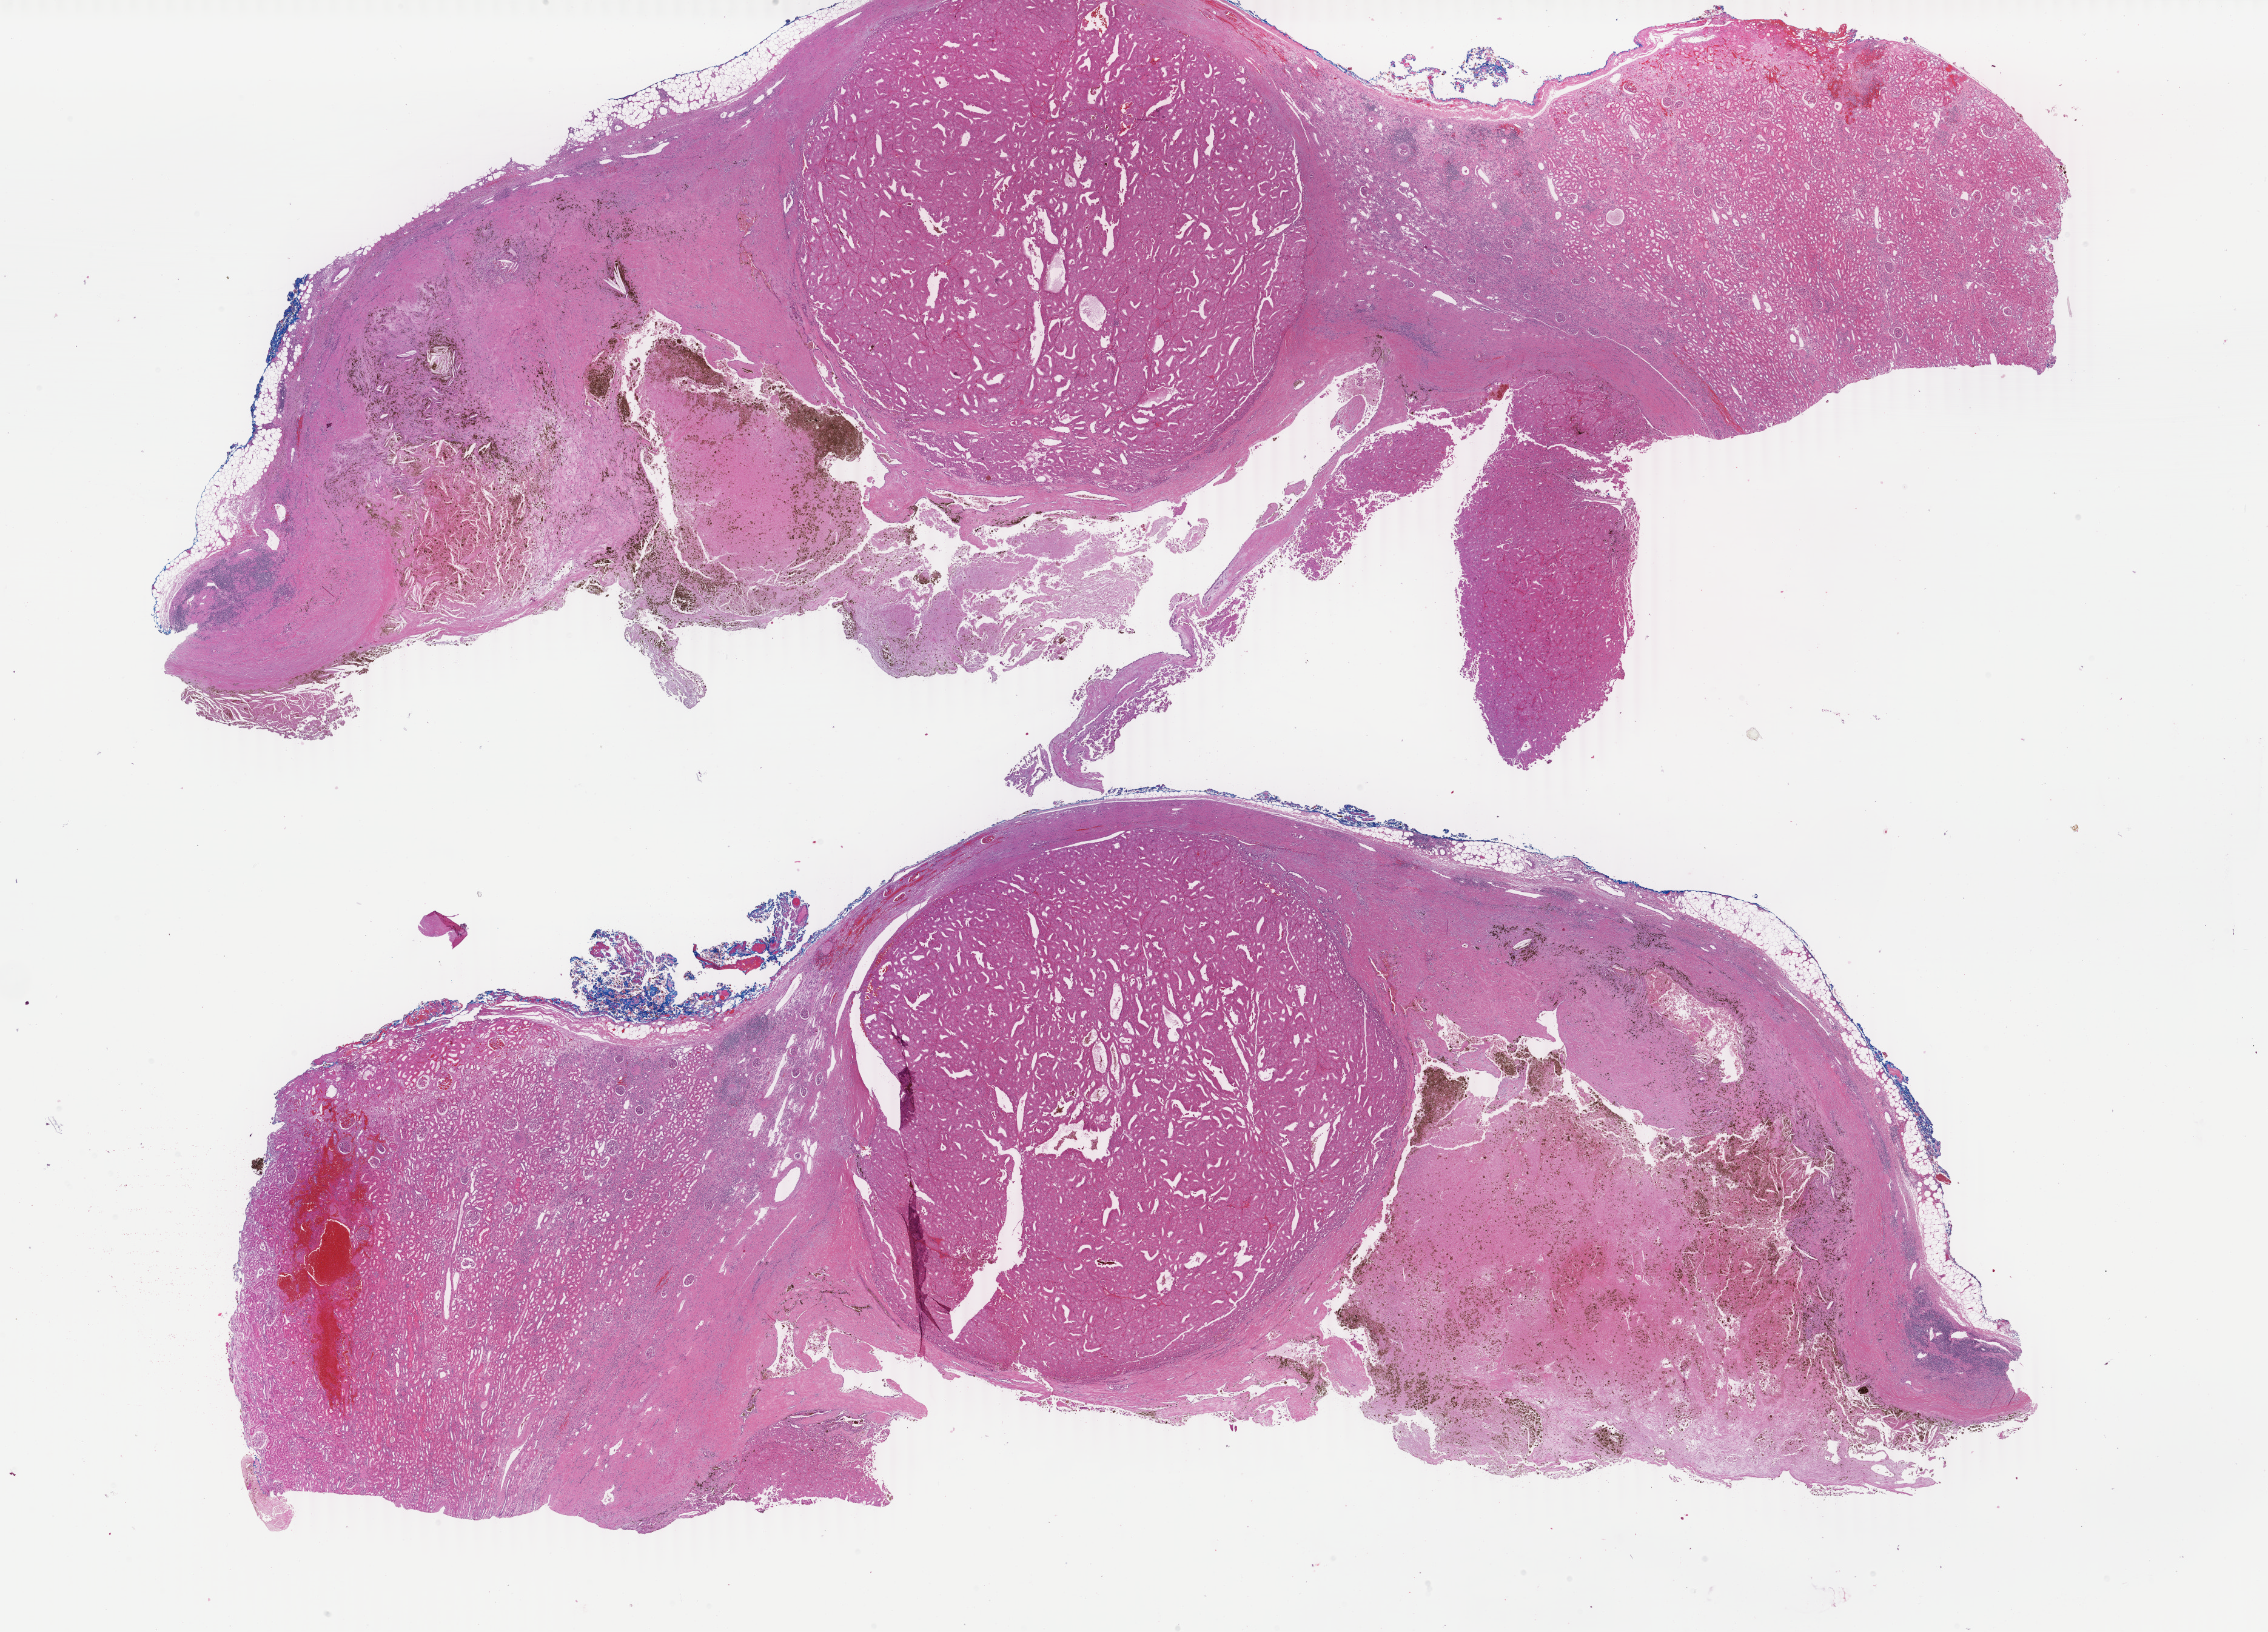
H&E whole-slide image, low-resolution overview of the scanned area, about 29.7 x 21.4 mm; FFPE section; primary tumour sample from the kidney. Patient: male, age at initial diagnosis 56 years.
- AJCC pathologic stage: I
- pathologic diagnosis: Renal cell carcinoma, chromophobe type